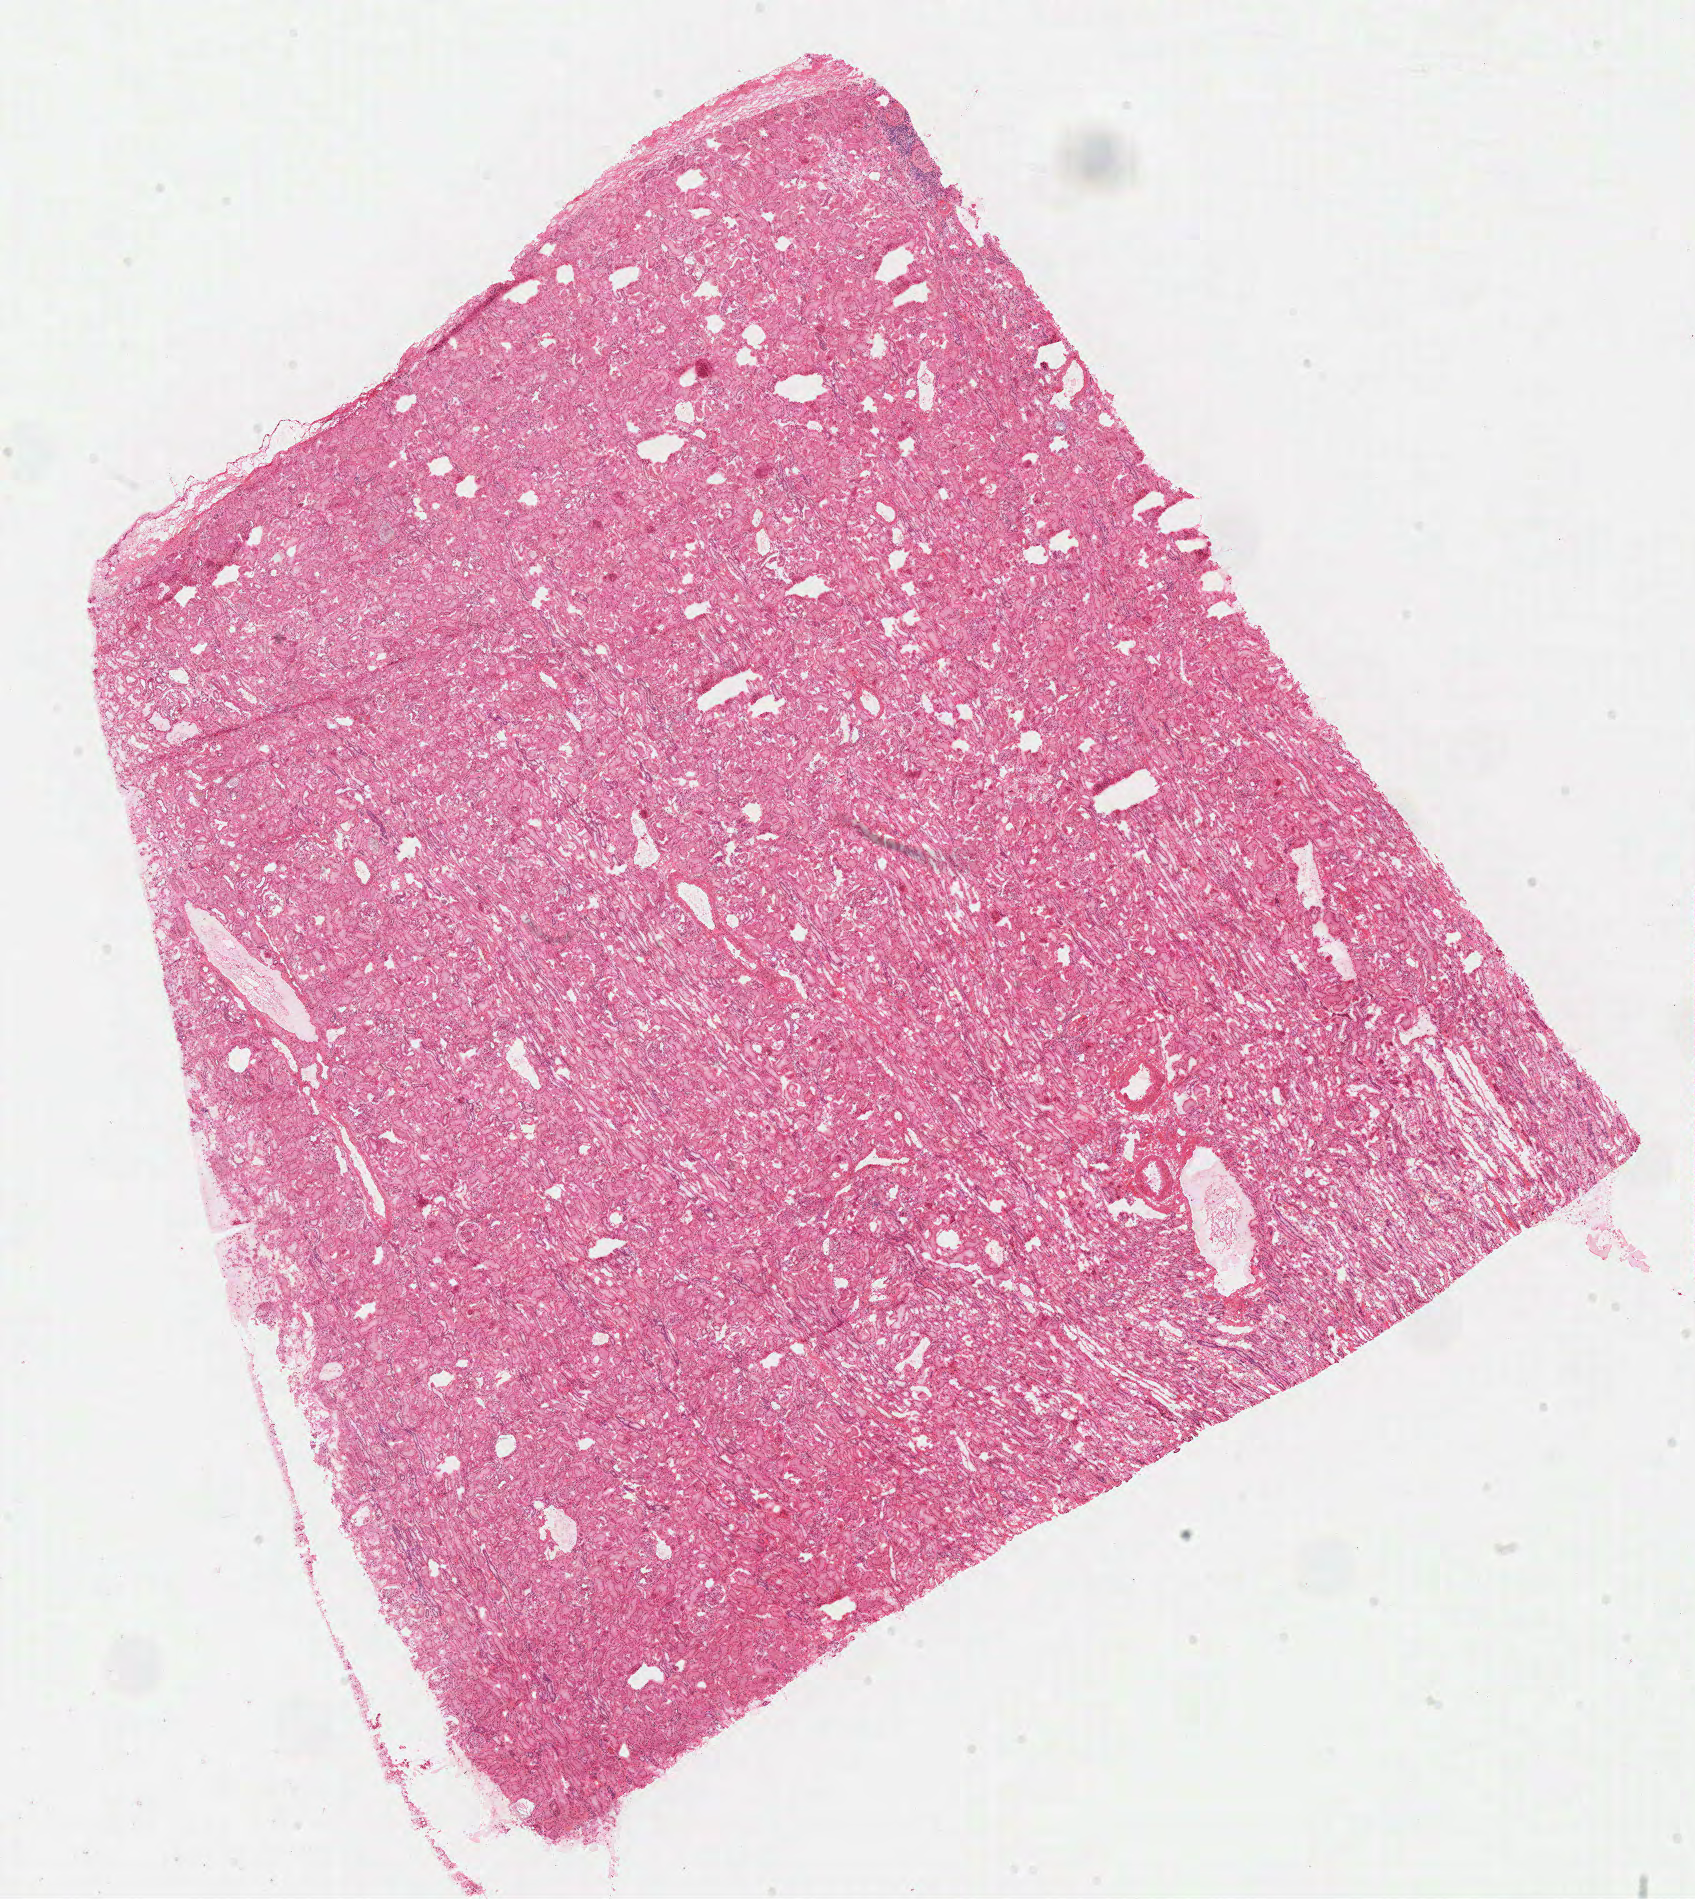
Hematoxylin and eosin (H&E) stained whole-slide image — whole scanned area (about 13.4 x 15.0 mm, acquisition: 40x scan) shown as a low-resolution overview; frozen section from the top of the tissue portion; sample: solid tissue normal (non-tumour tissue), kidney. Male patient; age at initial diagnosis 51 years.
This section: solid tissue normal sample (biorepository sample class). Patient diagnosis: Papillary adenocarcinoma, NOS.